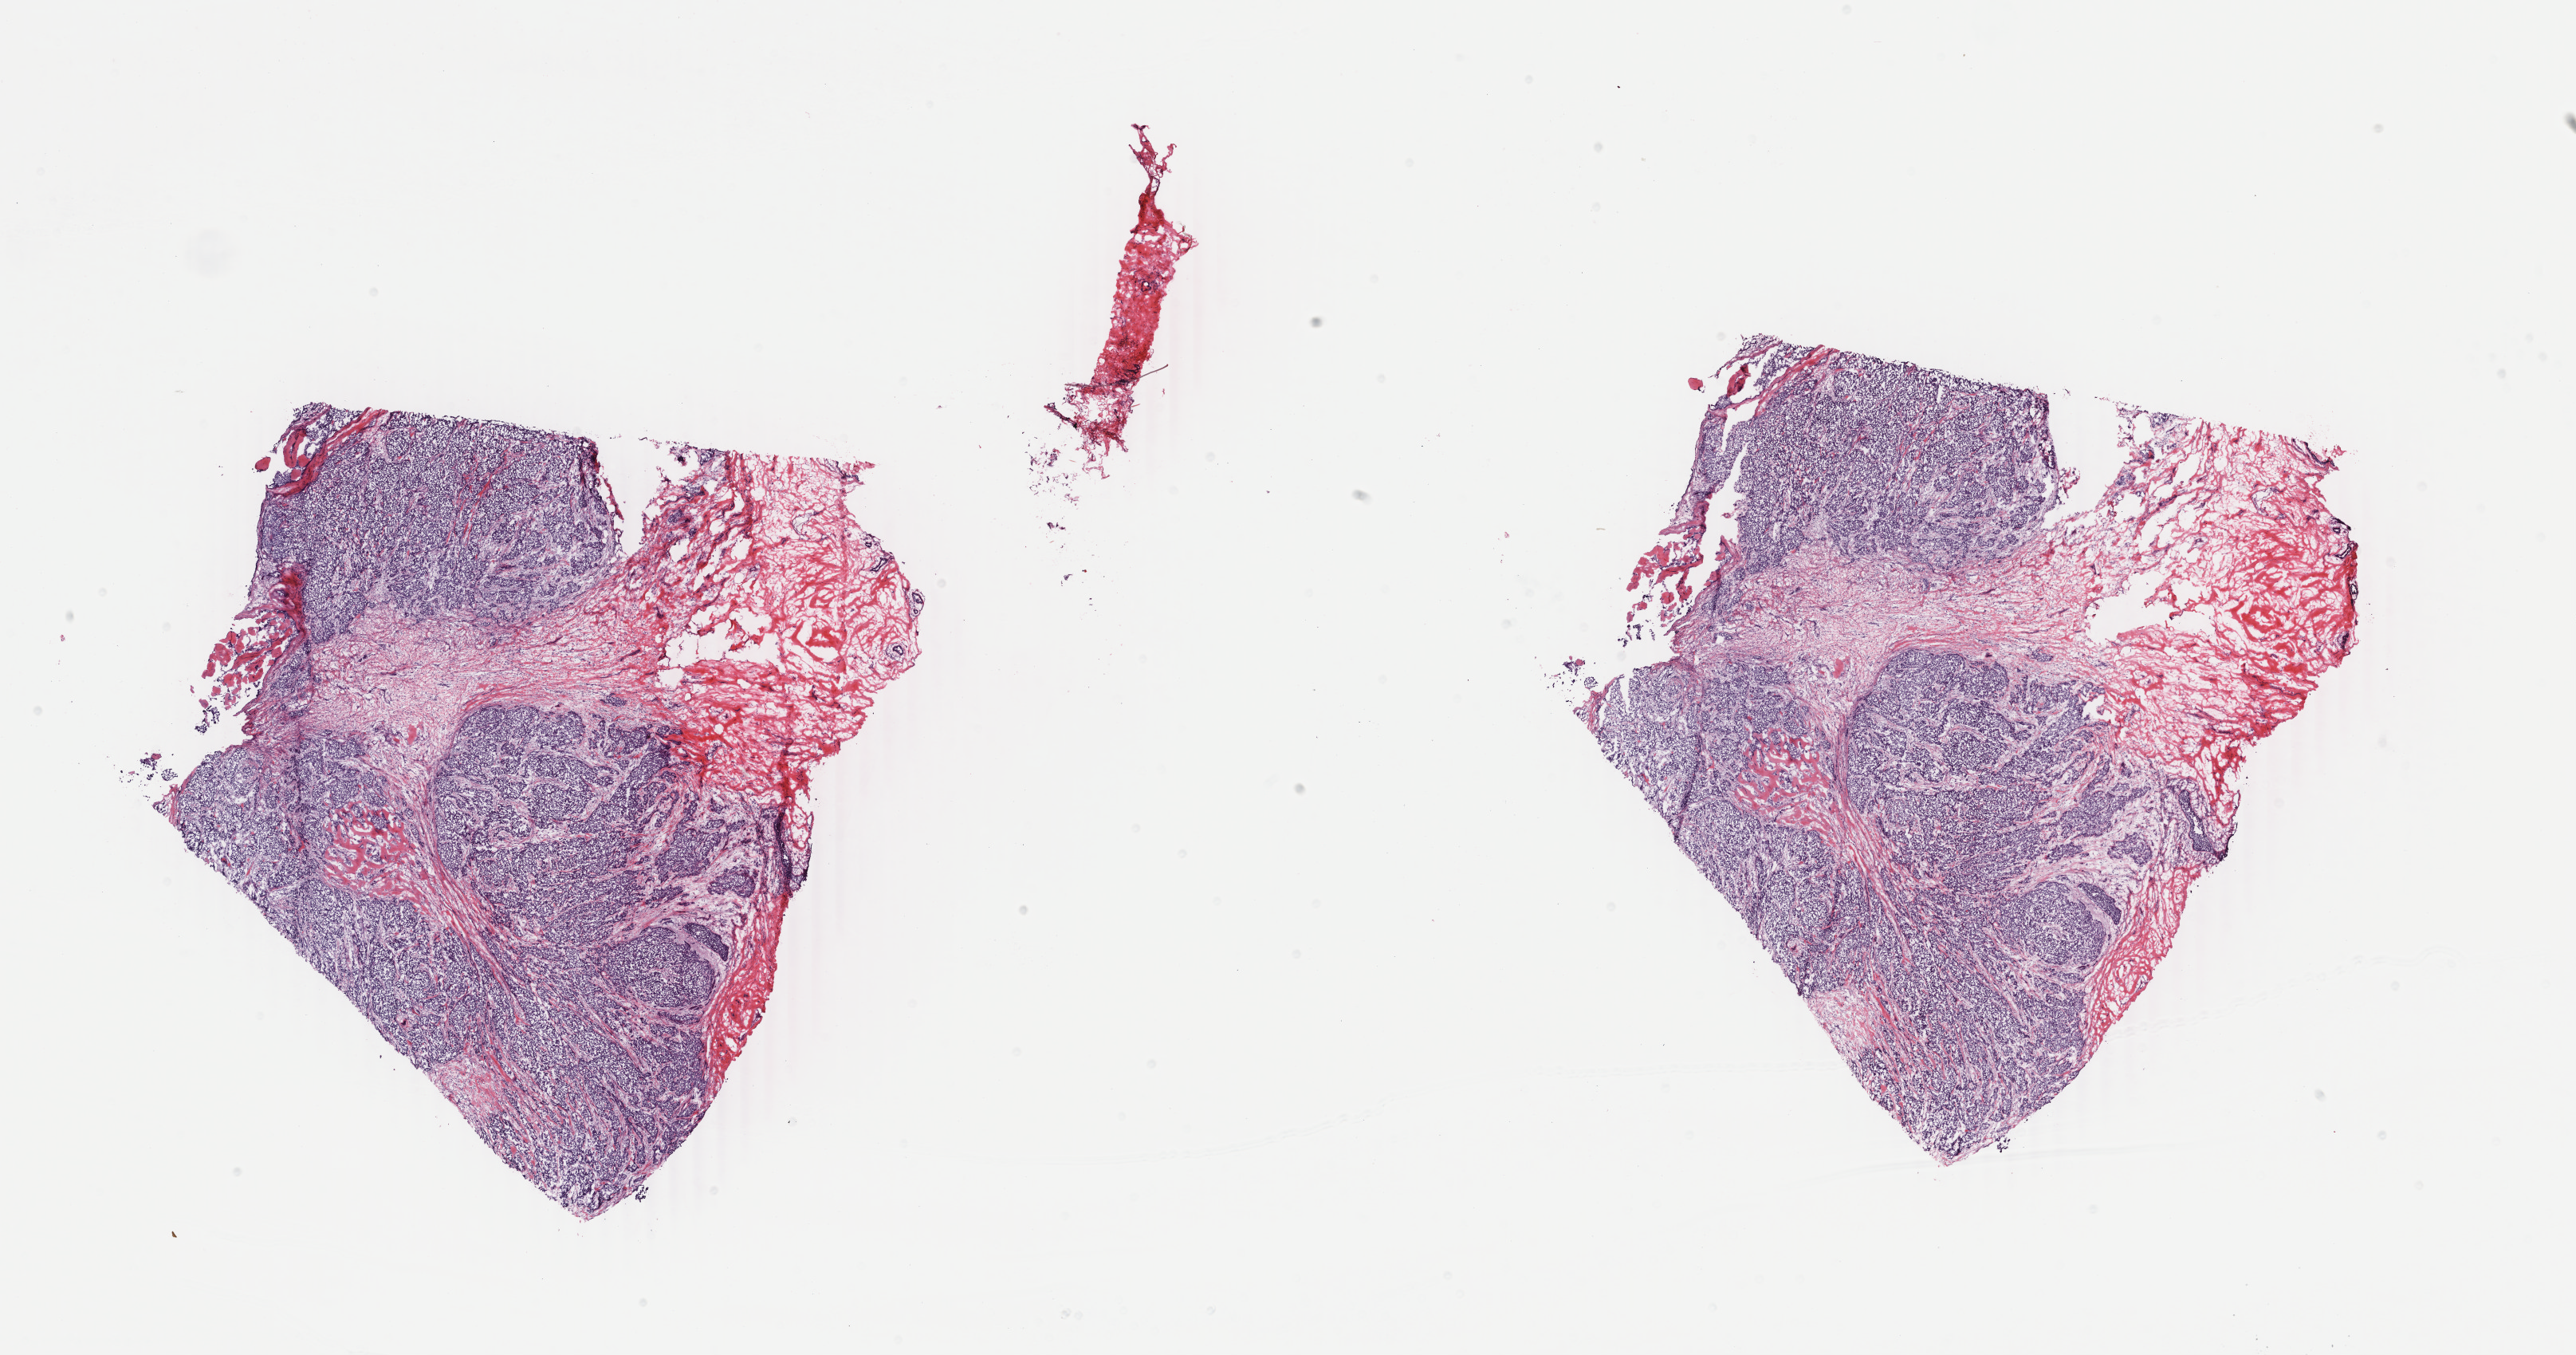
Whole-slide histology image, Hematoxylin and eosin (H&E) stained — a low-resolution overview of the entire scanned area, about 25.7 x 13.5 mm (slide scanned at 40x), frozen section from the bottom of the tissue portion, primary tumour sample from the breast. Female patient; age at initial diagnosis 66 years. Slide review estimates, as recorded: tumour cells 78%, tumour nuclei 88%, normal cells 2%, stromal cells 20%, necrosis 0%. Infiltration values recorded for this section: lymphocyte infiltration 1%, monocyte infiltration 0%, neutrophil infiltration 0%.
* lymph nodes positive (case pathology): 0 of 7 examined
* TNM: T2 N0 (i+) M0
* histologic diagnosis: Infiltrating duct carcinoma, NOS
* AJCC pathologic stage: IIA